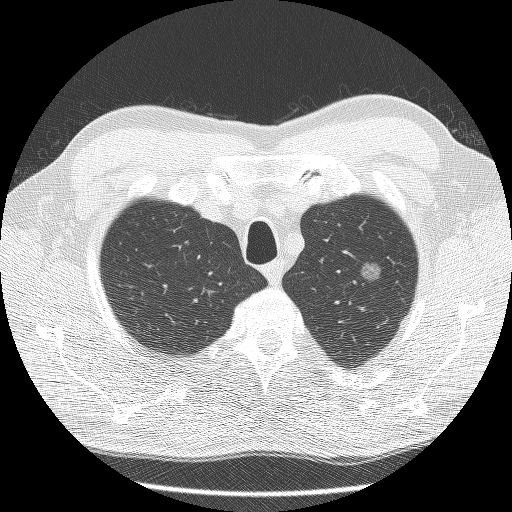
Chest CT (low-dose screening protocol), one axial image; third annual screen; lung window (W 1500 / L -600 HU); lung (sharp) reconstruction kernel (BONE). Male, age 60 years at enrolment.
• Expert-annotated lung lesion, bounding box <336,251,393,300> (left, top, right, bottom; pixels).
• The screening reader recorded 2 non-calcified nodules or masses ≥4 mm on this exam (right lower lobe, left upper lobe); which of them this box marks is not recorded.
• Official screen result: positive, other.